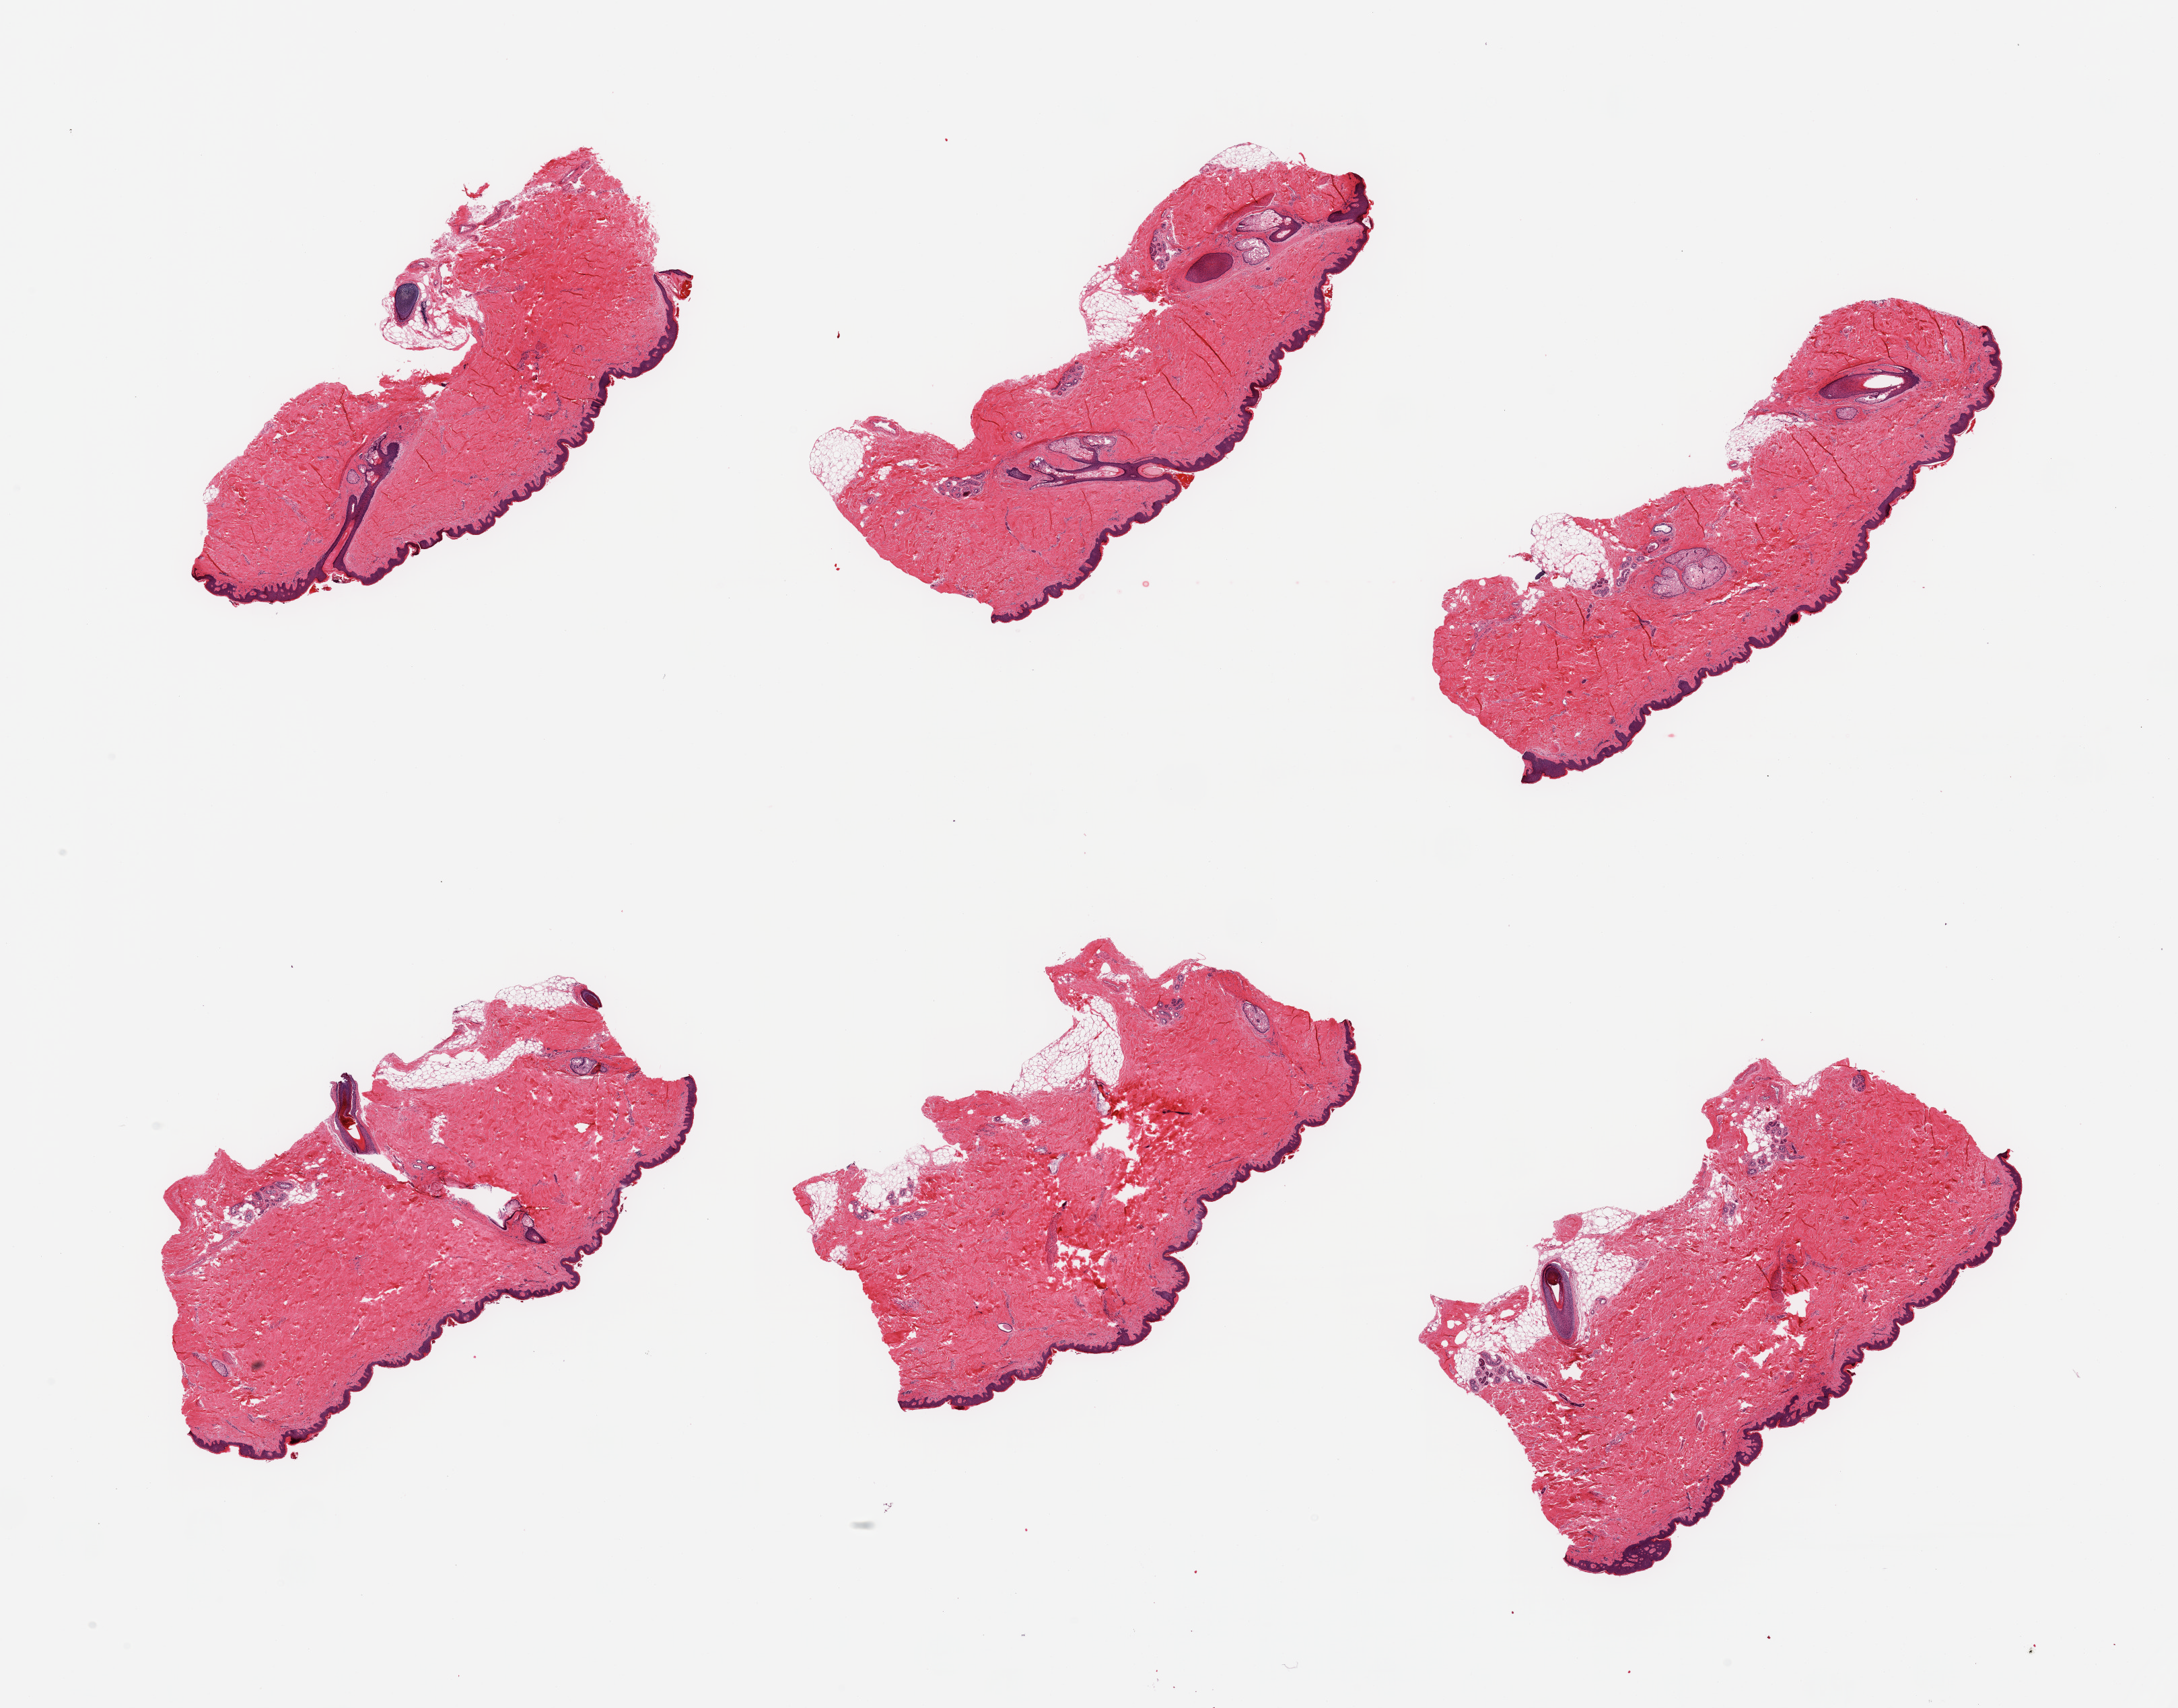
Whole-slide image, haematoxylin and eosin stain, brightfield, whole scanned area (about 25.6 x 20.1 mm, from a 20x scan) shown as a low-resolution overview; PAXgene-fixed paraffin-embedded (PFPE) section; sampled site (target tissue): skin of suprapubic region; tissue donor sample. Donor: male.
Reviewer comment on this tissue sample: 6 pieces; trimmed but up to 10% fat still remain.